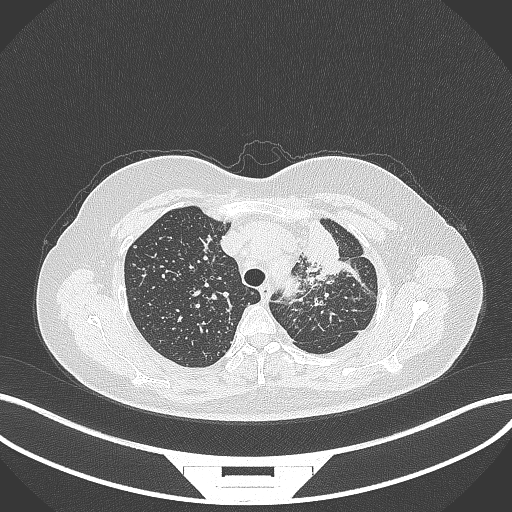
Chest CT, one axial slice; slice 262 of 348 in the series (ordered by position); reconstruction kernel B70f; 120 kVp; lung window (W 1500 / L -600 HU); 1 mm slice thickness; 512 × 512 image matrix. Female patient, age 49 years. Case-level facts recorded for this patient, not image findings: clinical TNM (as recorded): T1c N0 M1.
Structures marked on this image (rectangle marked by the reading radiologist):
- lung tumour (recorded histology: adenocarcinoma): bounding box <299,211,348,278> (left, top, right, bottom; pixels)